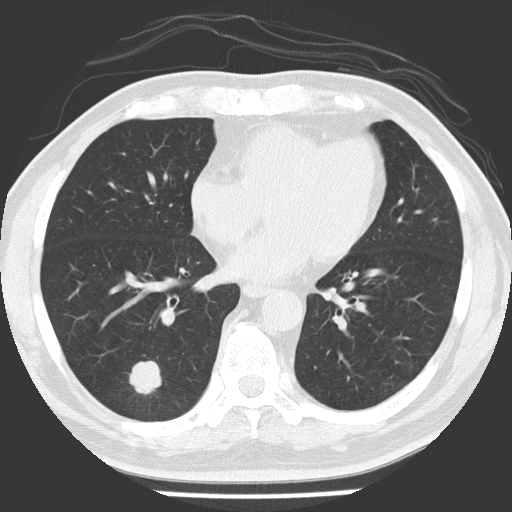
Axial slice from a low-dose chest CT screening exam; baseline annual screen; lung window (W 1500 / L -600 HU); 2 mm slice thickness; 120 kVp; slice 89 of 154 in the series; 512 × 512 image matrix. Male, age 56 years at enrolment. Former smoker at enrolment.
Lesion marked by an expert reader, bounding box (x1, y1, x2, y2) in pixels: (116, 352, 168, 404). The exam's reader record, not a measurement of the box and not confirmed to be the same lesion: non-calcified nodule or mass ≥4 mm, right lower lobe, 21 × 17 mm, spiculated (stellate) margins, soft tissue attenuation. Official screen result: positive, change unspecified: nodule(s) >= 4 mm or enlarging nodule(s), mass(es), or other non-specific abnormalities suspicious for lung cancer. Lung cancer was diagnosed 84 days after this screen: adenocarcinoma, NOS, right lower lobe, poorly differentiated (G3), stage IA (AJCC 6th edition), 24 mm at pathology.